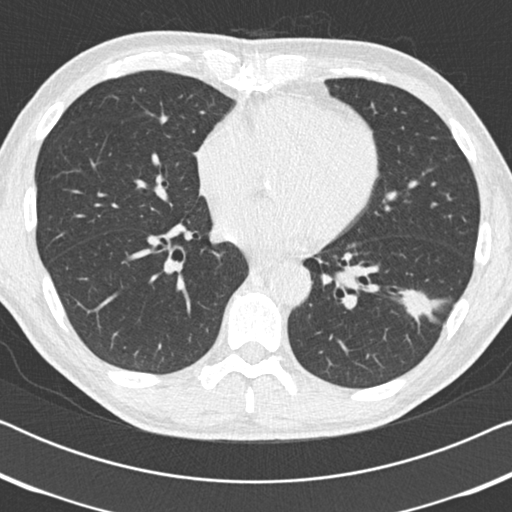
Low-dose screening chest CT, one axial slice. Slice 80 of 186 in the series (ordered by position). 120 kVp. Lung window (W 1500 / L -600 HU). 2 mm slice thickness. 512 × 512 image matrix.
Outlined on this slice (outlined manually by an expert reader):
- lesion 1 (tumor, lower lobe of left lung): box from (x=402, y=293) to (x=434, y=317) px